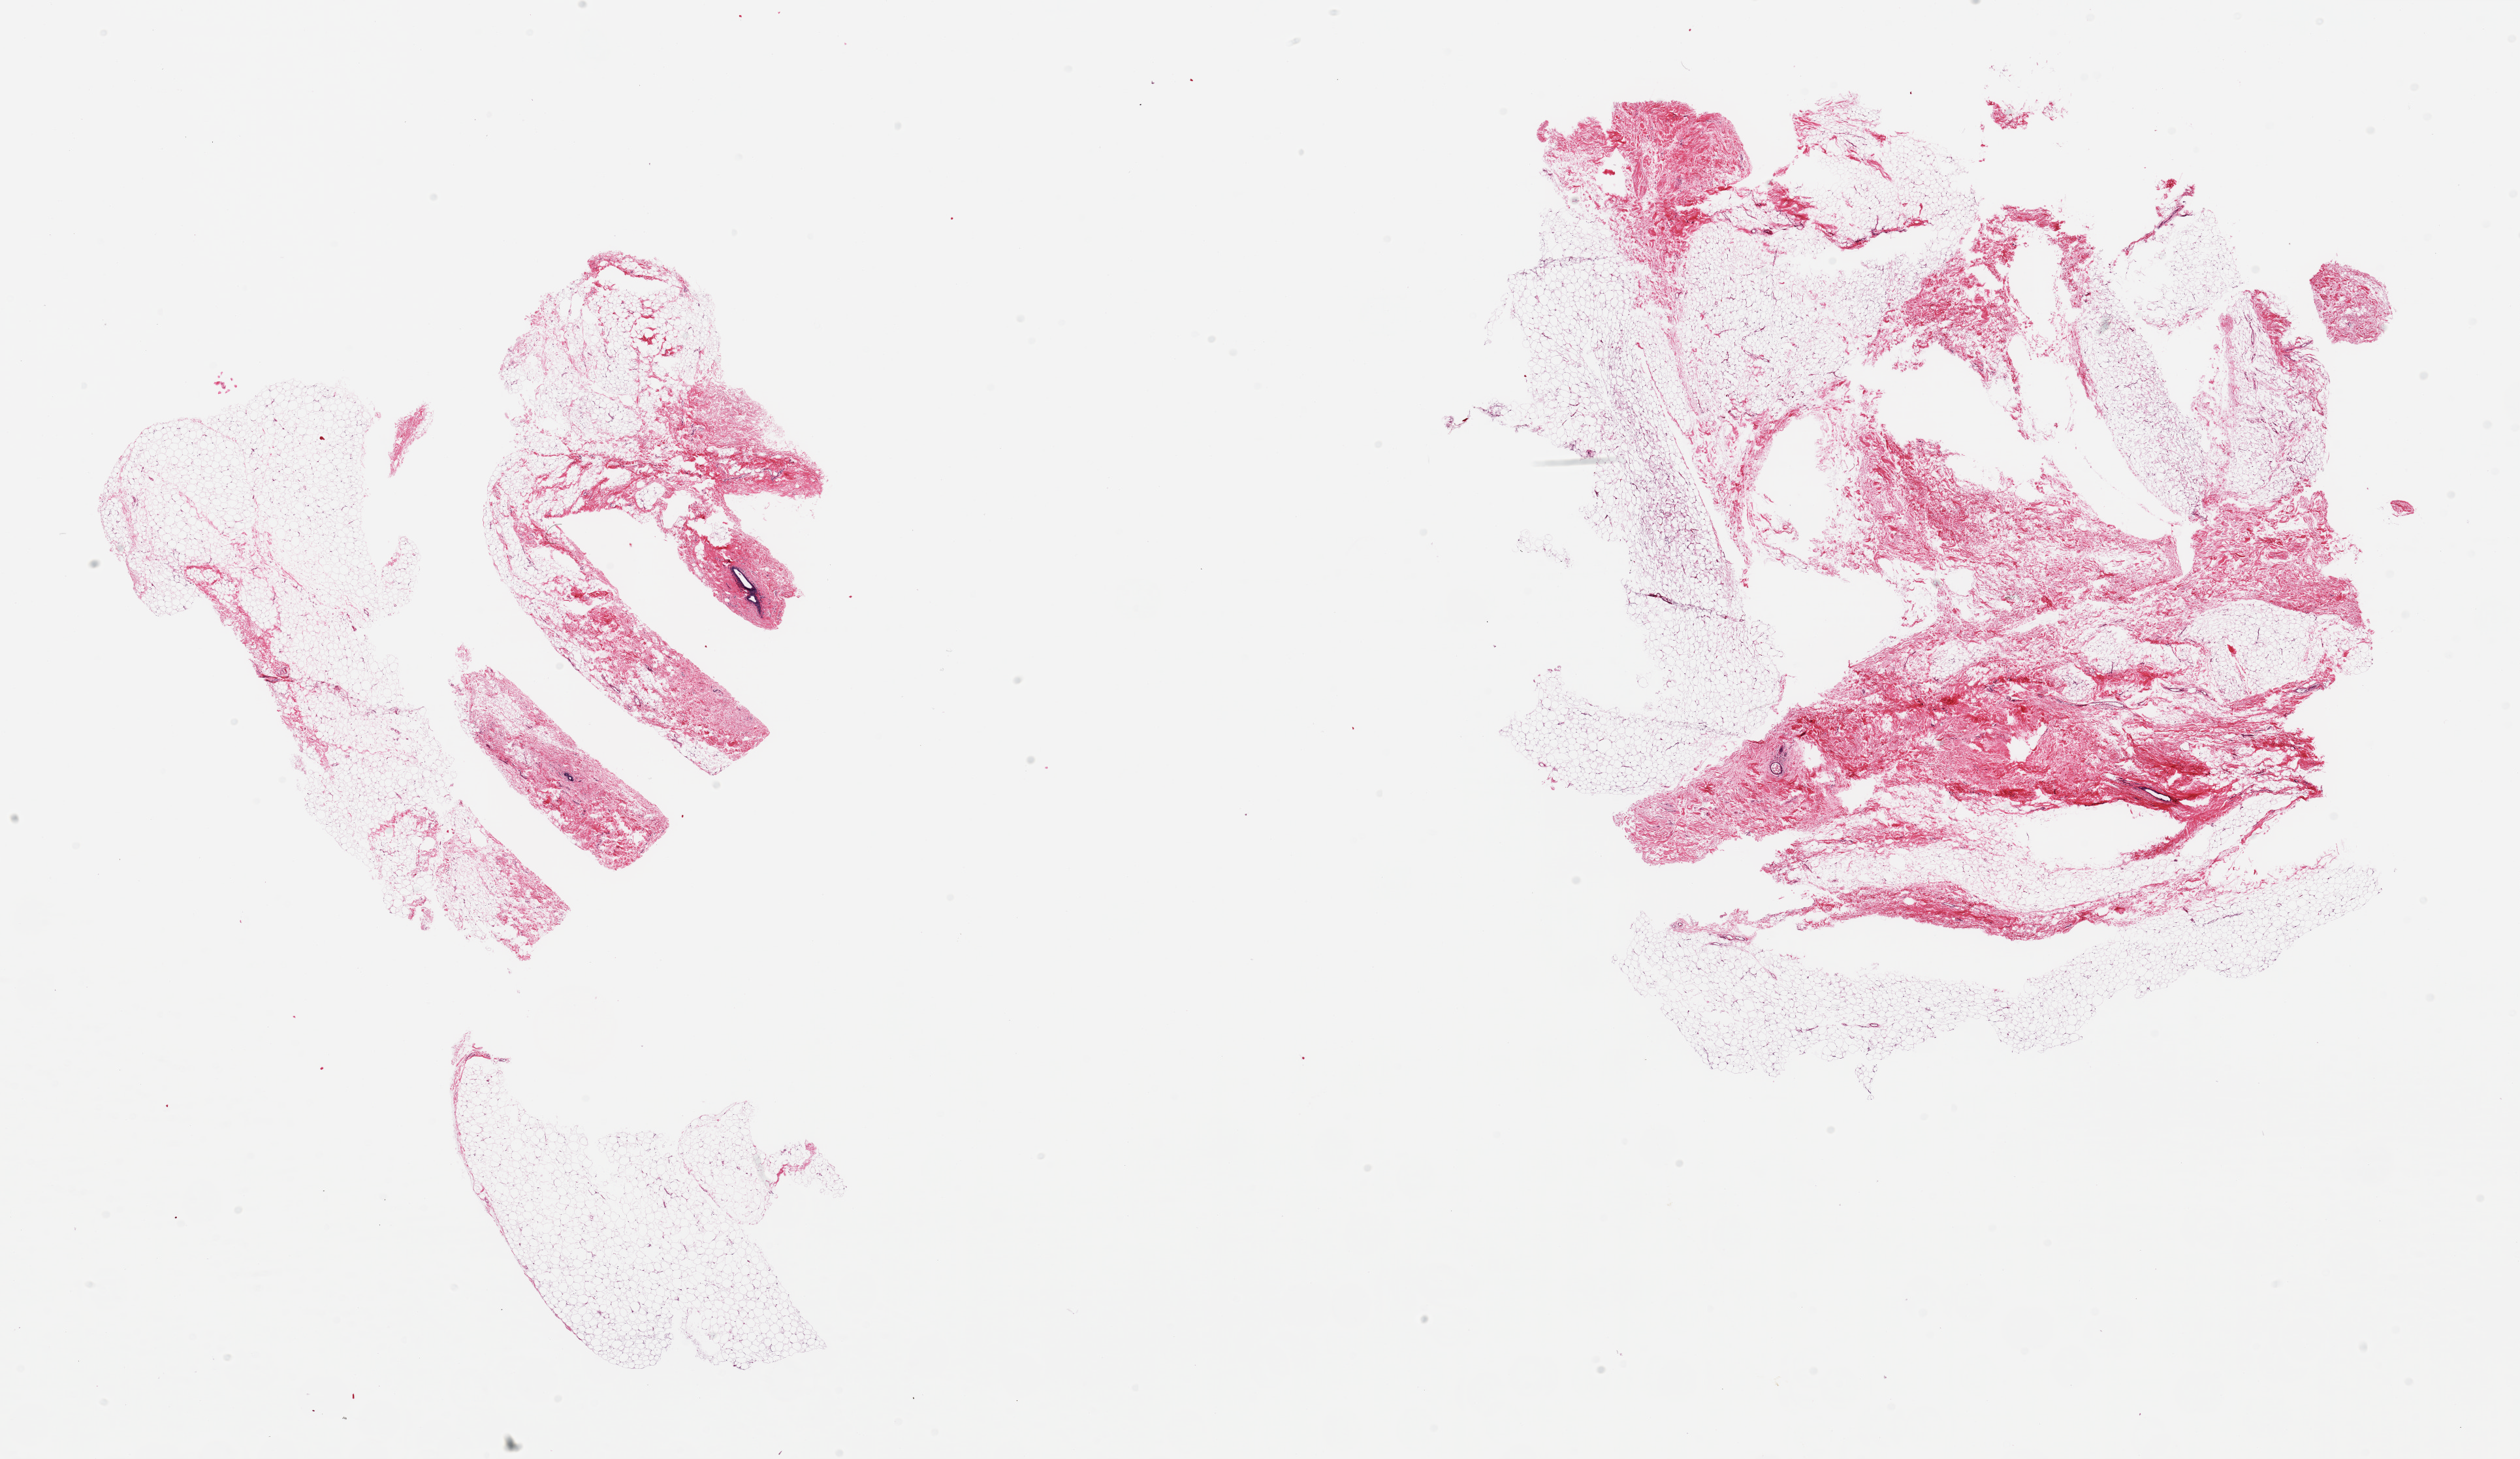
Whole-slide image, haematoxylin and eosin stain — shown as a low-resolution overview of the whole scanned area (about 30.5 x 17.7 mm, acquisition: 20x scan). PAXgene-fixed, paraffin-embedded tissue. Target tissue: breast. Tissue donor sample. Female donor.
Review note (as recorded): 2 pieces; several atrophic ducts in fibrofatty tissue.